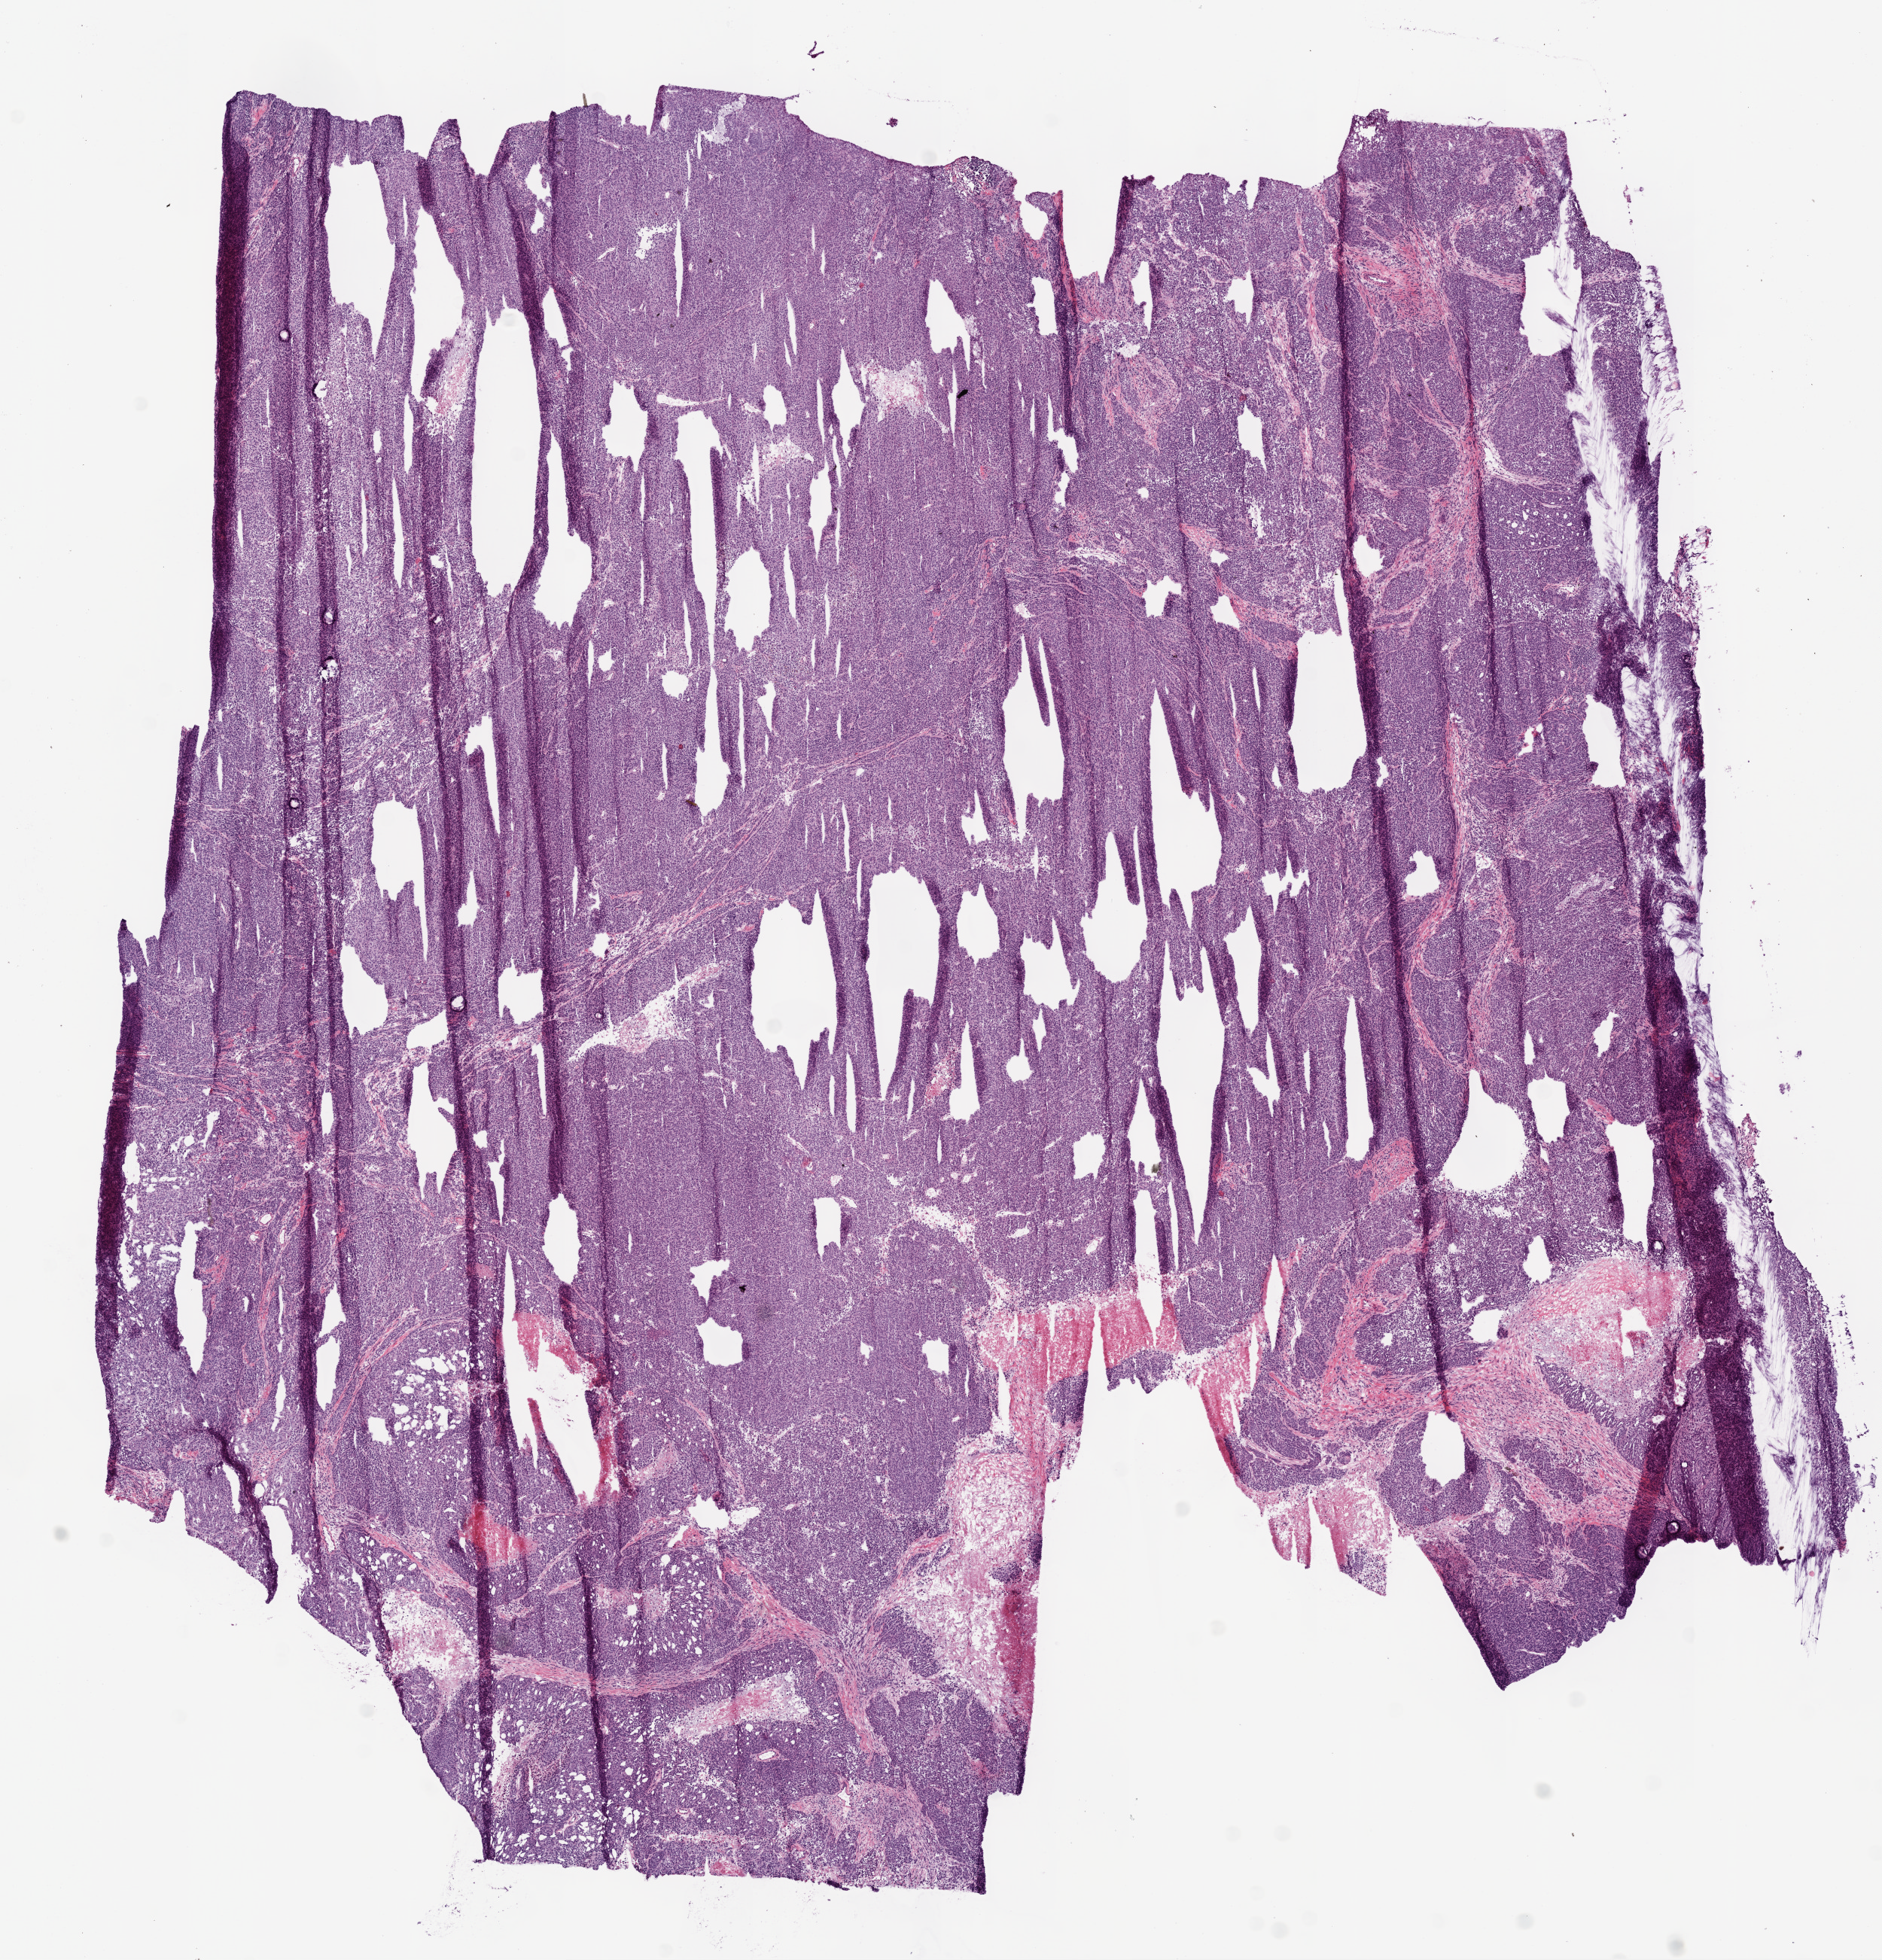
Whole-slide histology image, Hematoxylin and eosin (H&E) stained — shown as a low-resolution overview of the whole scanned area (about 10.0 x 10.4 mm); frozen section from the bottom of the tissue portion; ovary, primary tumour sample. Female patient; age at initial diagnosis 72 years.
Histologic diagnosis: Serous cystadenocarcinoma, NOS.